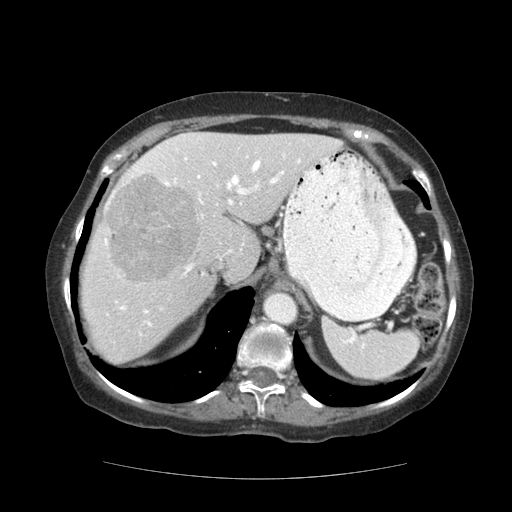
Contrast-enhanced abdominal CT (liver protocol), one axial slice; slice 85 of 111 in the series (ordered by position); reconstruction kernel STANDARD; 140 kVp; soft-tissue window (W 400 / L 40 HU); 2.5 mm slice thickness; 512 × 512 image matrix, field of view 360 × 360 mm. From the clinical record (not read from this slice): diagnosis: hepatocellular carcinoma (patient treated with transarterial chemoembolisation; whether this scan precedes or follows treatment is not stated here); TNM stage (as recorded): Stage-I; Child-Pugh class: A; tumour differentiation: moderately-poorly differentiated; tumour size: 7.3 cm.
Structures marked on this image (semi-automatic segmentation, software-assisted and operator-edited):
- liver parenchyma outside the tumour (the mass and vessels are separate outlines, so this box may not span the whole liver): box from (x=82, y=132) to (x=342, y=364) px
- mass: (x=103, y=174)–(x=203, y=283)
- liver vessels: (x=104, y=135)–(x=337, y=335)